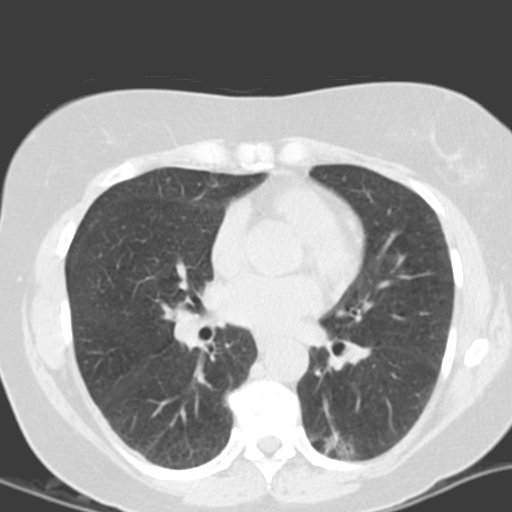
Low-dose screening chest CT, axial slice, second screening round (one year after baseline), lung window (W 1500 / L -600 HU), standard (soft-tissue) reconstruction kernel (B). Female, age 55 years at enrolment. Current smoker at enrolment.
Lesion marked by an expert reader, box from (x=305, y=411) to (x=379, y=467) px. The screening reader recorded 4 non-calcified nodules or masses ≥4 mm on this exam; which of them this box marks is not recorded. Official screen result: positive, other. Participant outcome: lung cancer diagnosed 688 days after this screen (after the third annual screen) — adenocarcinoma with mixed subtypes, left lower lobe, poorly differentiated (G3), stage IA (AJCC 6th edition), 21 mm at pathology.